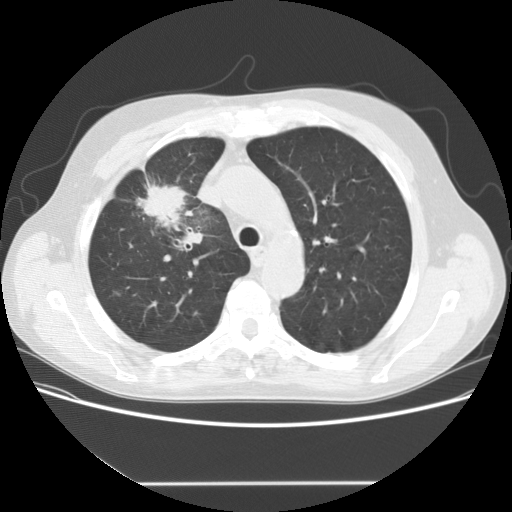
Low-dose screening chest CT, axial slice. Baseline annual screen. Lung window (W 1500 / L -600 HU). 2.5 mm slice thickness. Standard (soft-tissue) reconstruction kernel (STANDARD). Slice 41 of 153 in the series. Male participant, aged 56 years at enrolment.
- Expert reader's lesion annotation, bounding box <127,171,215,248> (left, top, right, bottom; pixels).
- The screening reader recorded 2 non-calcified nodules or masses ≥4 mm on this exam; which of them this box marks is not recorded.
- Later outcome: lung cancer diagnosed 120 days after this screen — adenocarcinoma, NOS, right upper lobe, stage IIIA (AJCC 6th edition), 34 mm at pathology.